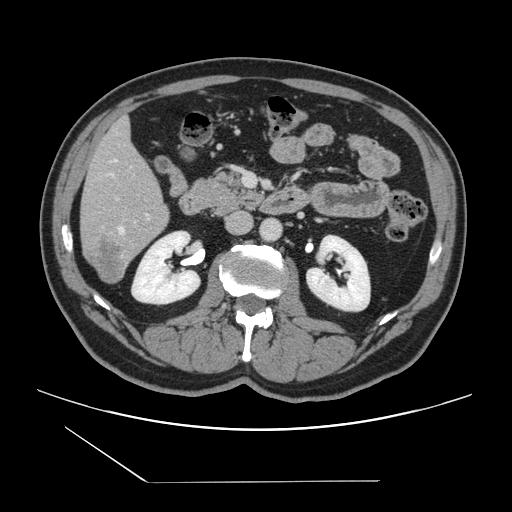
Contrast-enhanced abdominal CT, one axial slice; position 54 of 157 along the scan axis; 120 kVp; intravenous contrast given; soft-tissue window (W 400 / L 40 HU); 512 × 512 image matrix. Male patient, age 61 years. From the clinical record (not read from this slice): diagnosis: colorectal cancer liver metastases, imaged before liver resection; multiple liver metastases: yes; largest metastasis: 5.5 cm; chemotherapy before resection: no.
Structures marked on this image (expert manual segmentation):
- hepatic veins: bounding box <112,159,124,233> (left, top, right, bottom; pixels)
- liver: <81,120,169,283>
- planned liver remnant (the part of the liver to remain after resection): <82,121,165,218>
- portal vein (with intrahepatic branches): <116,197,150,219>
- liver metastasis: <89,238,125,282>